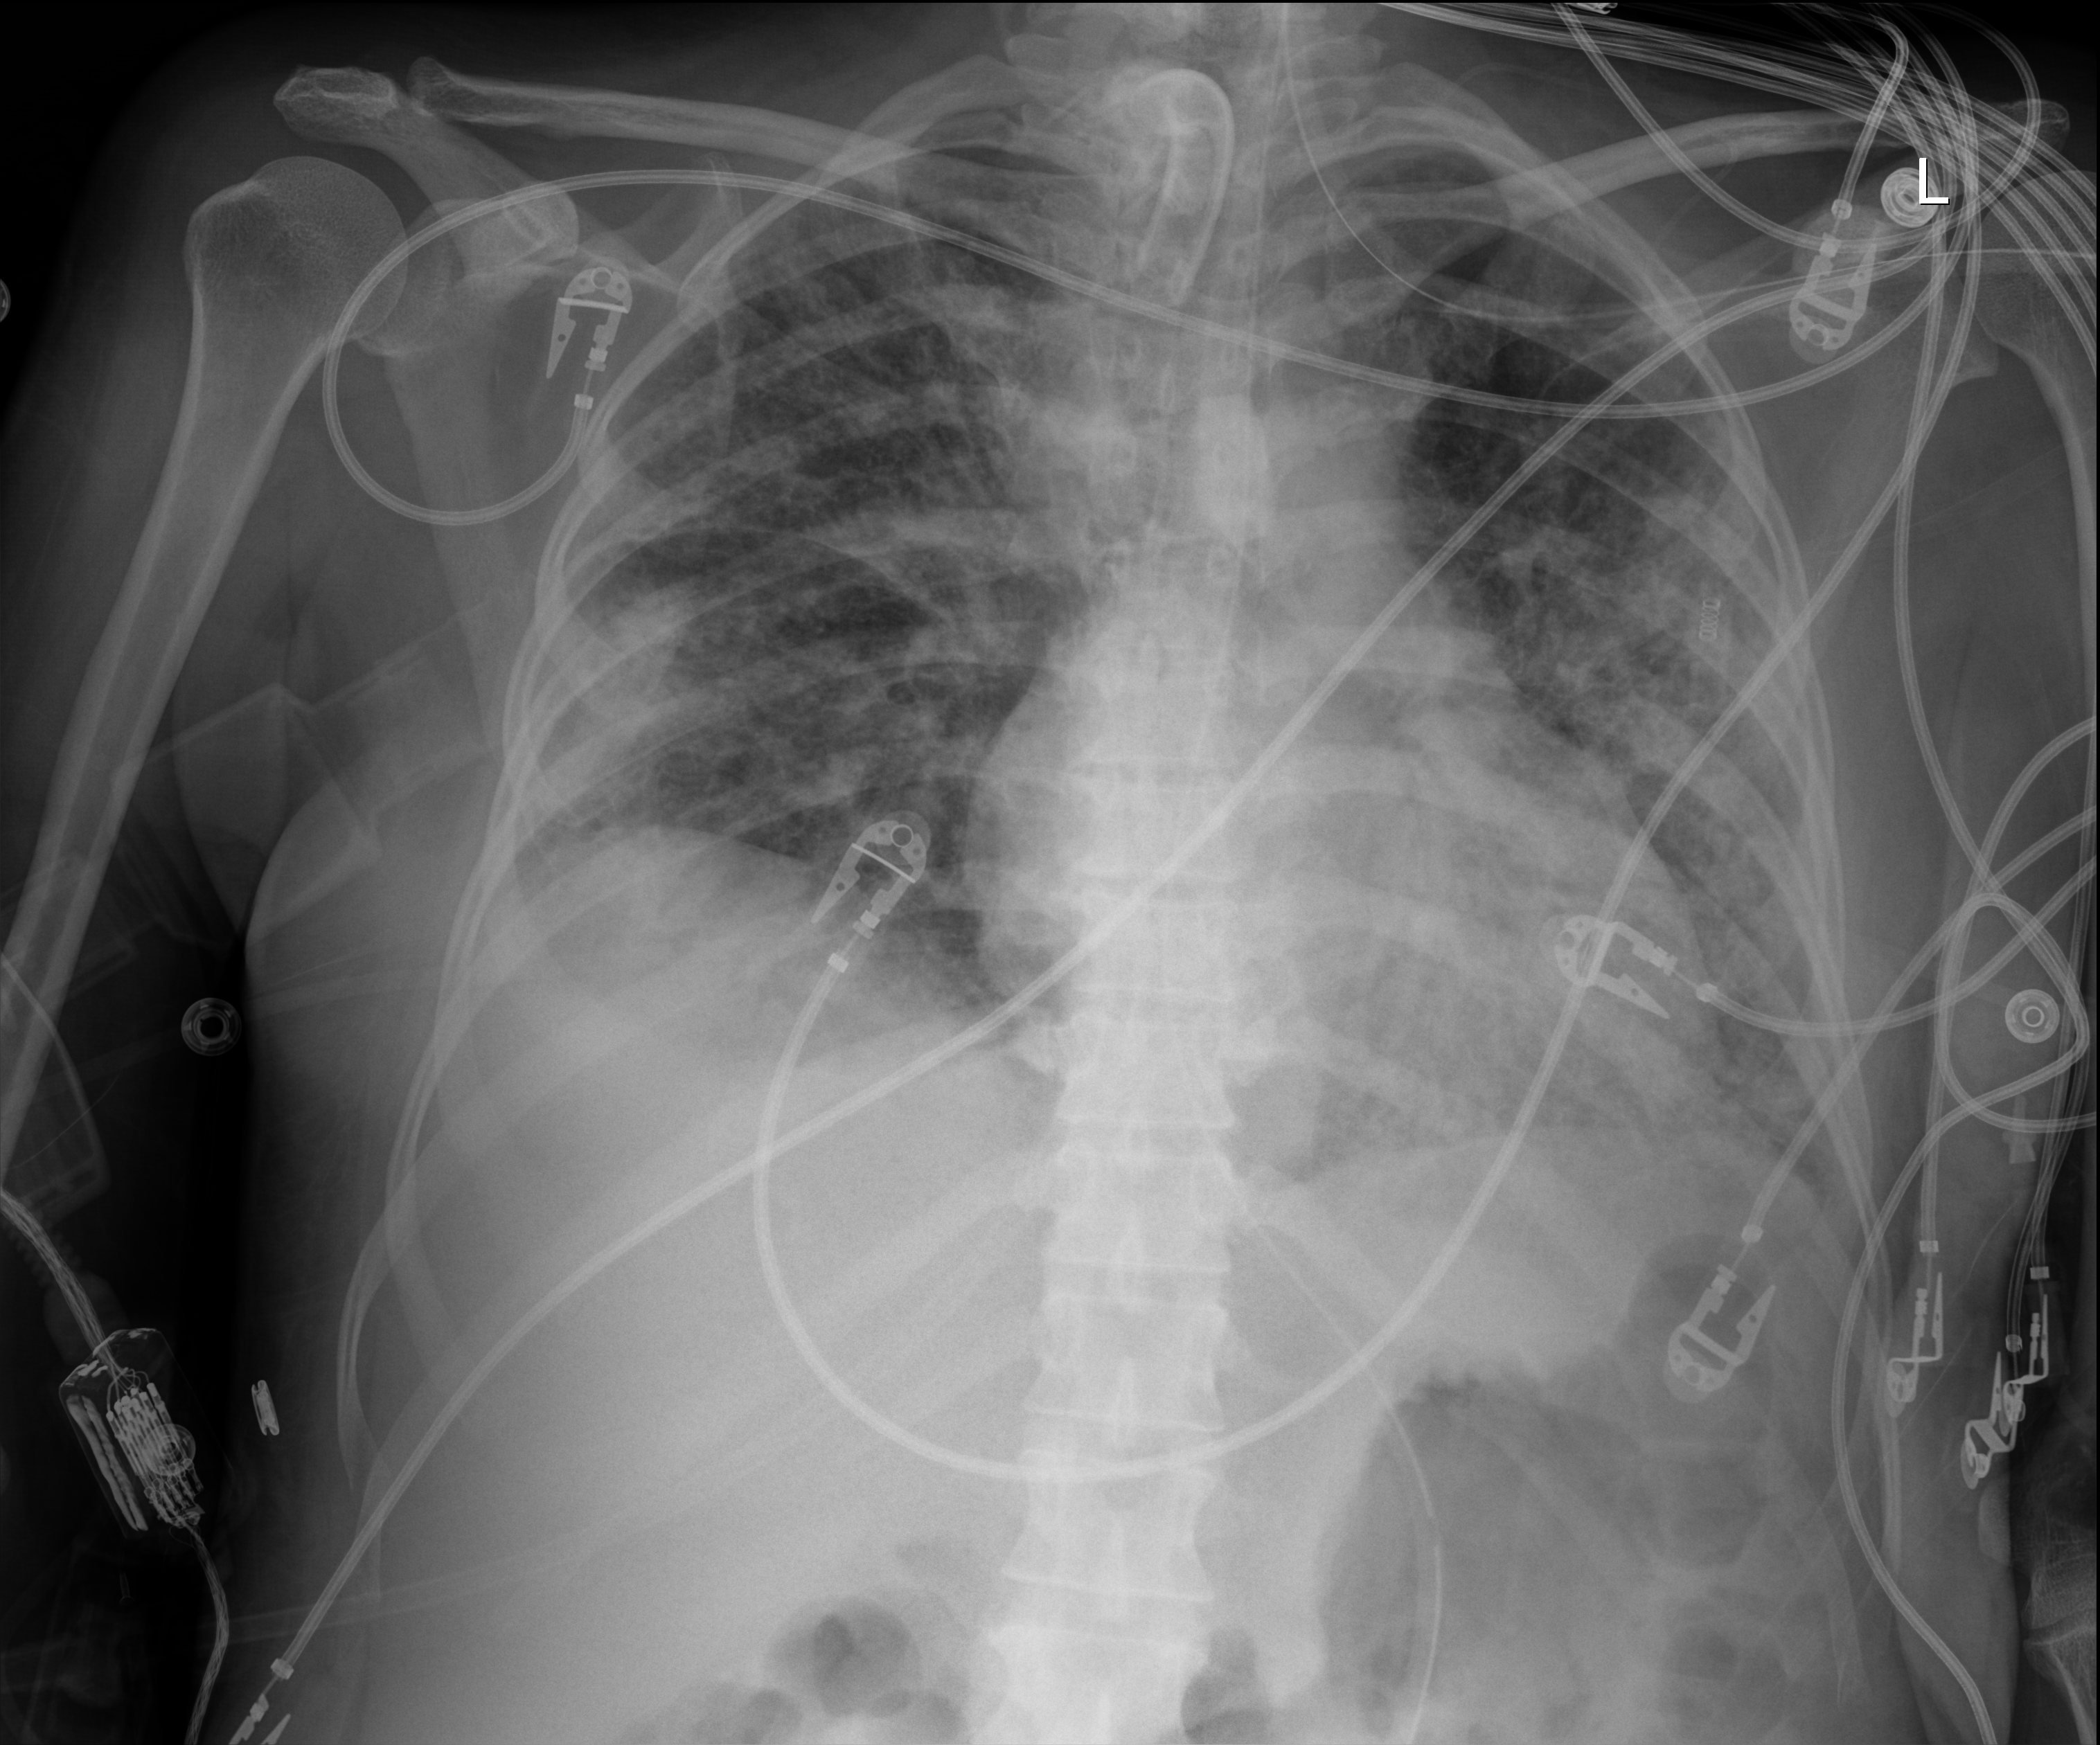
Portable chest radiograph; anteroposterior (AP) projection. Female patient hospitalised with COVID-19, age 18–59 years.
Admission-level facts for this patient (not findings on this image; timing relative to this image not recorded):
- other chronic lung disease (admission record): no
- mechanically ventilated during this hospital stay: yes
- admitted to intensive care during this hospital stay: yes